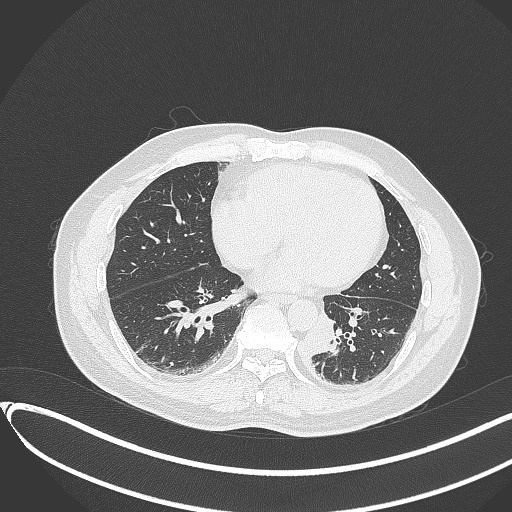
Chest CT, one axial slice. Slice 121 of 417 in the series (ordered by position). Reconstruction kernel B70f. 120 kVp. Lung window (W 1500 / L -600 HU). 1 mm slice thickness. 512 × 512 image matrix, field of view 400 × 400 mm. Patient: male, 54 years. From the clinical record (not read from this slice): clinical TNM (as recorded): T3 N0 M0.
Annotated regions visible in this slice (rectangle marked by the reading radiologist):
- lung tumour (recorded histology: squamous cell carcinoma): bounding box (x1, y1, x2, y2) in pixels: (298, 305, 337, 361)